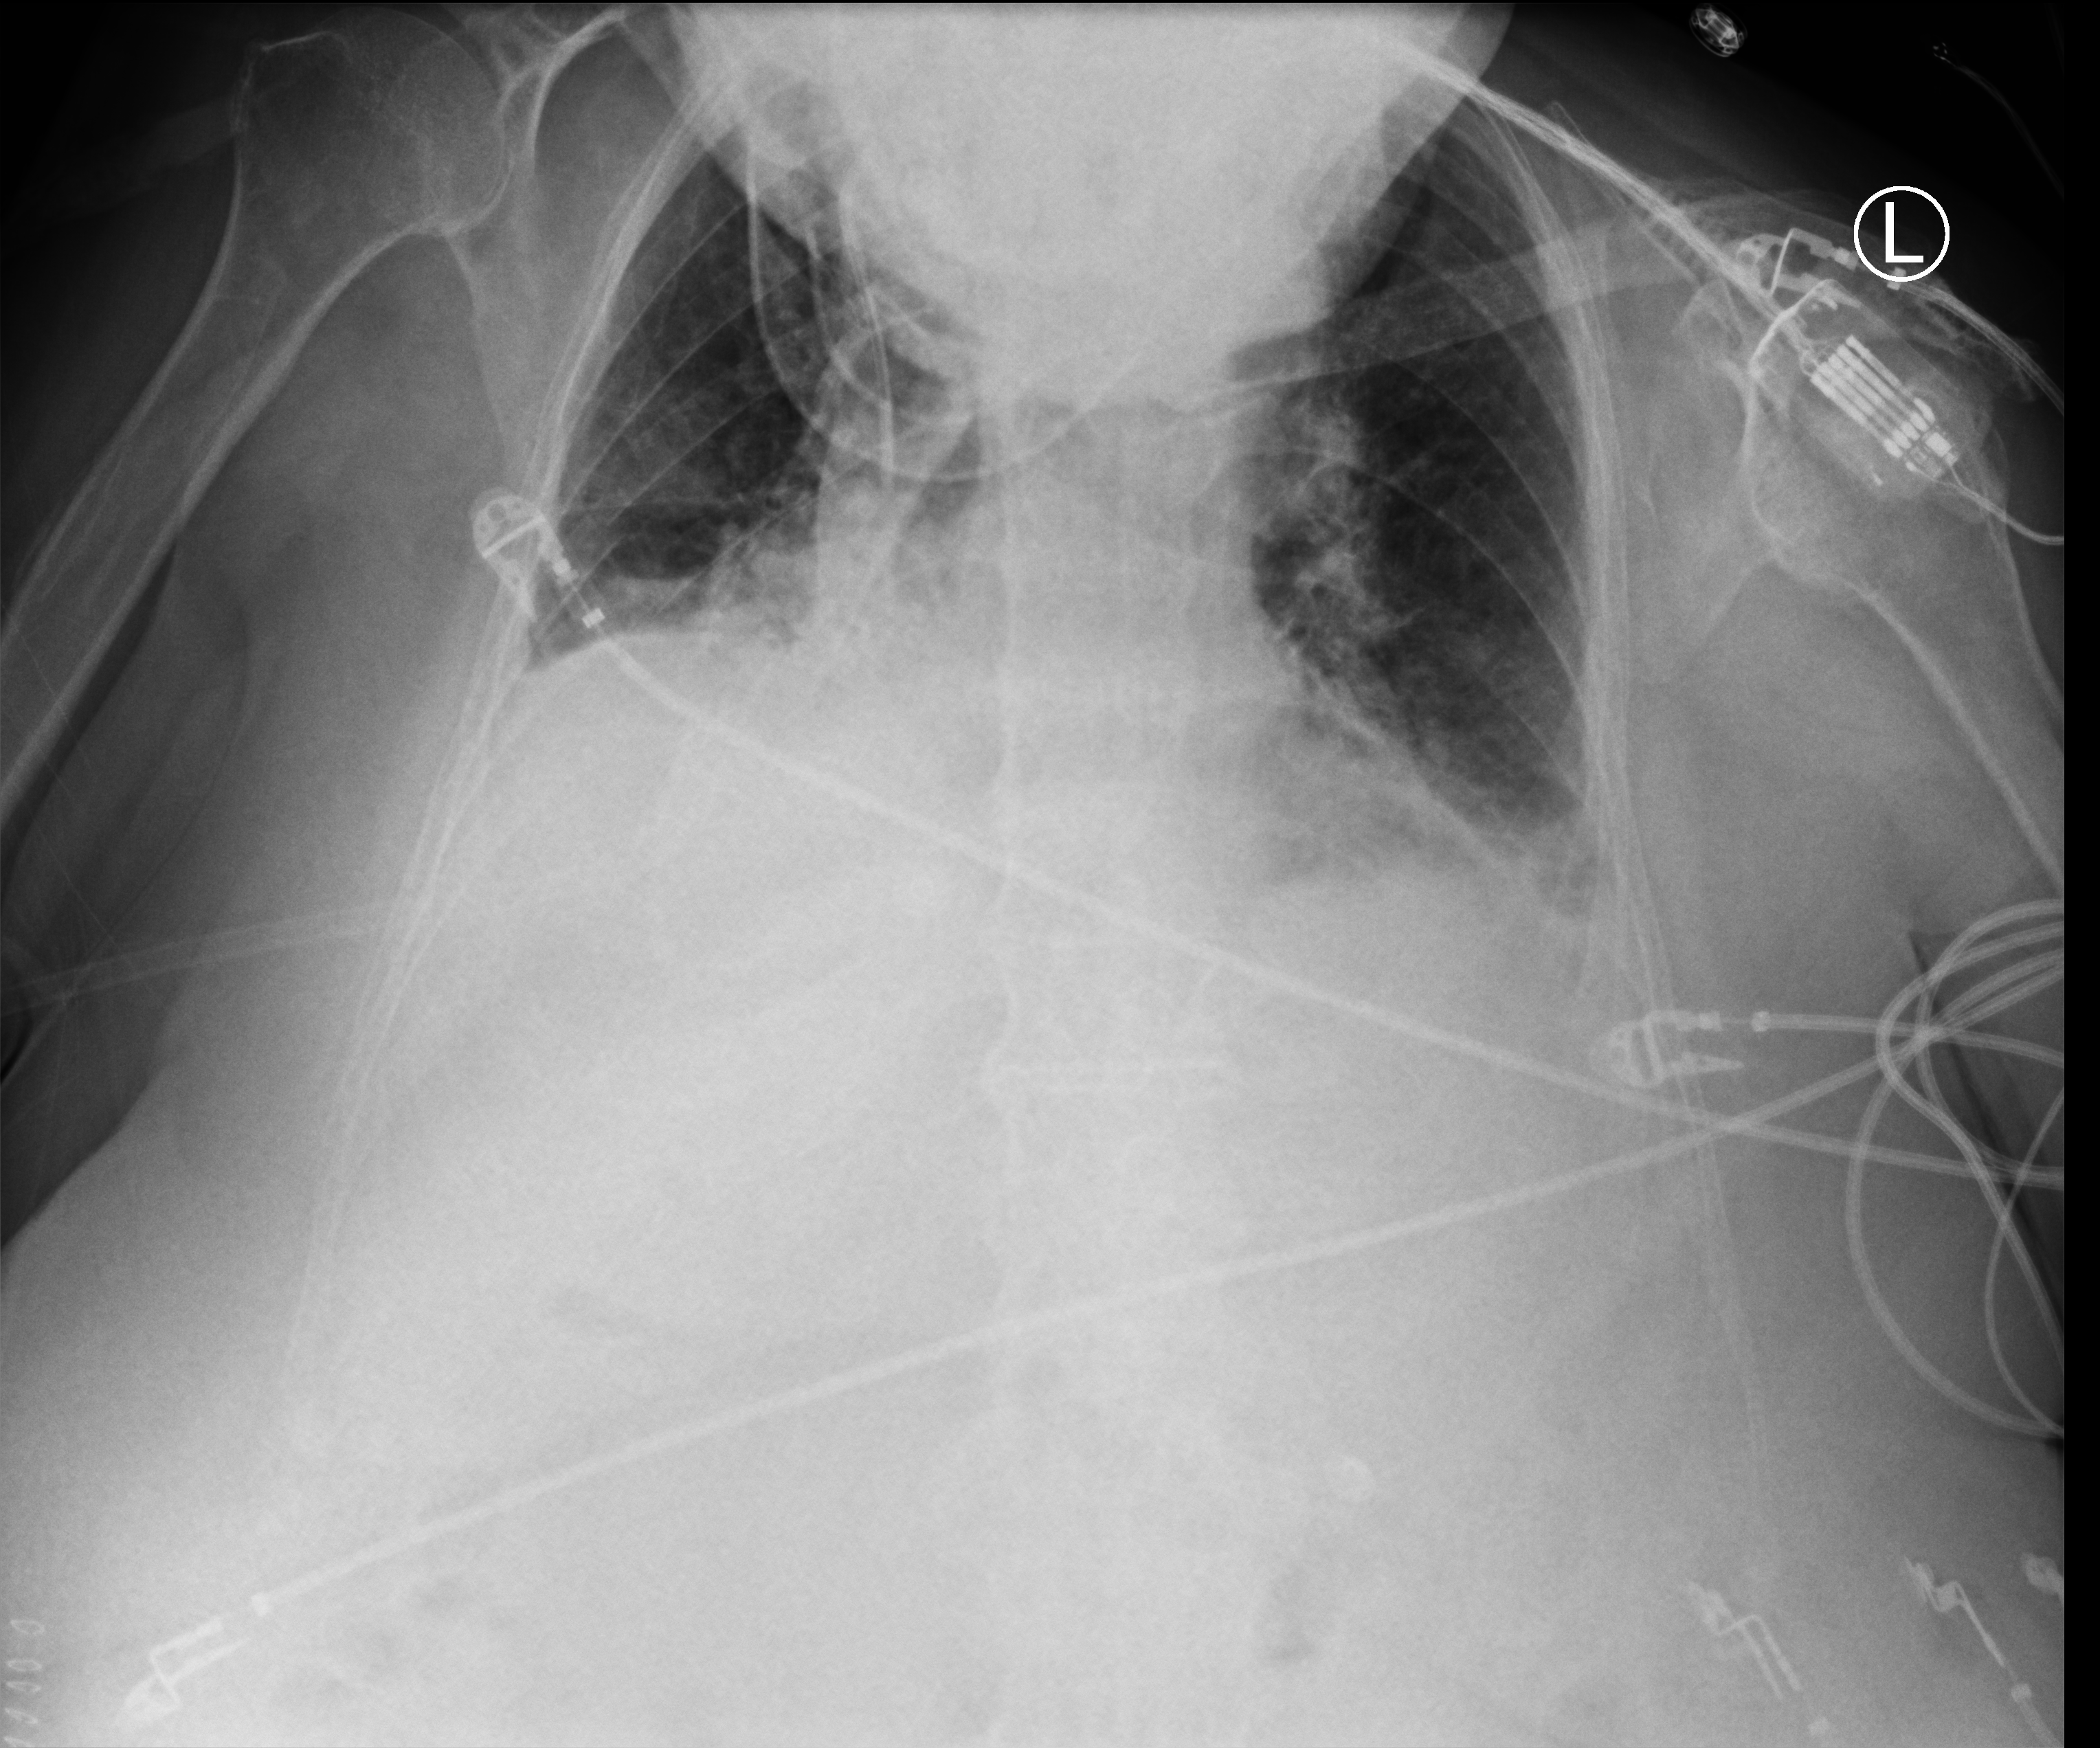
Portable chest radiograph; anteroposterior (AP) projection. Patient hospitalised with COVID-19; female, aged 75–90 years.
Hospital-stay facts (about this admission, not read from this image; timing relative to this image not recorded): mechanically ventilated during this hospital stay: yes; diabetes (admission record): no.